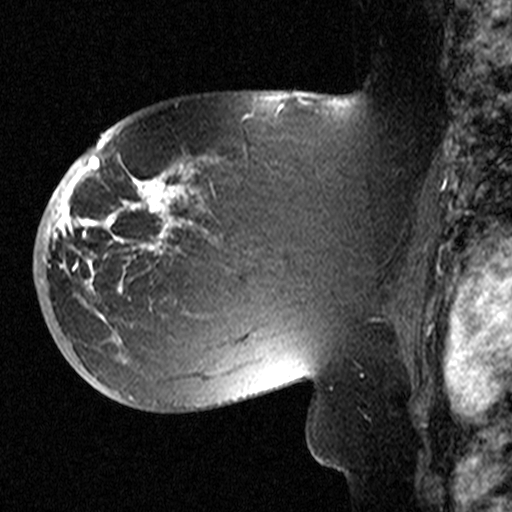
Breast MRI (dynamic contrast-enhanced), one sagittal slice; slice 28 of 44 in the series (ordered by position); dynamic contrast-enhanced study with each time point stored as its own series, time point 2 of 3 at this slice position (early post-contrast, ordered by acquisition time); 1.5 T; TE 4.5 ms, TR 11 ms; 3.27 mm slice thickness; 512 × 512 image matrix, field of view 200 × 200 mm. Female patient, age 53 years. From the clinical record (not read from this slice): setting: breast cancer imaged before/during neoadjuvant chemotherapy; receptor status: HR-positive, HER2-negative.
Outlined on this slice (semi-automatic segmentation, software-assisted and operator-edited):
- analysis volume of interest (the breast-tissue region the enhancement analysis was run in; not a lesion): box from (x=58, y=154) to (x=311, y=367) px
- tumour enhancement mask (voxels above the 90 % enhancement threshold inside the analysis volume of interest): (x=58, y=167)–(x=193, y=342)